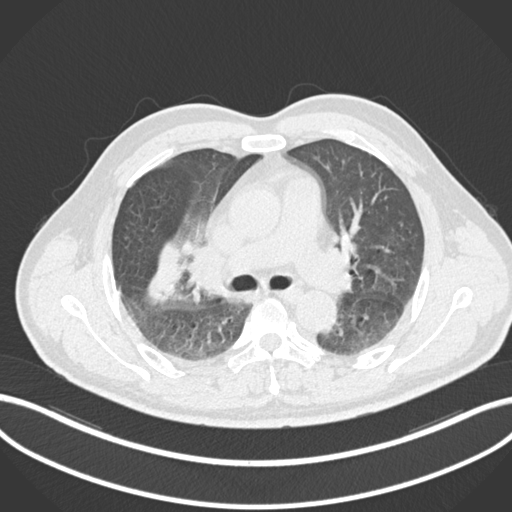
Chest CT, one axial slice; slice 640 of 852 in the series (ordered by position); lung window (W 1500 / L -600 HU); 1 mm slice thickness; 512 × 512 image matrix, field of view 400 × 400 mm. Male patient, age 55 years. From the clinical record (not read from this slice): clinical TNM (as recorded): T3 N2 M1.
Structures marked on this image (rectangle marked by the reading radiologist):
- lung tumour (recorded histology: adenocarcinoma): bounding box (x1, y1, x2, y2) in pixels: (142, 238, 185, 303)